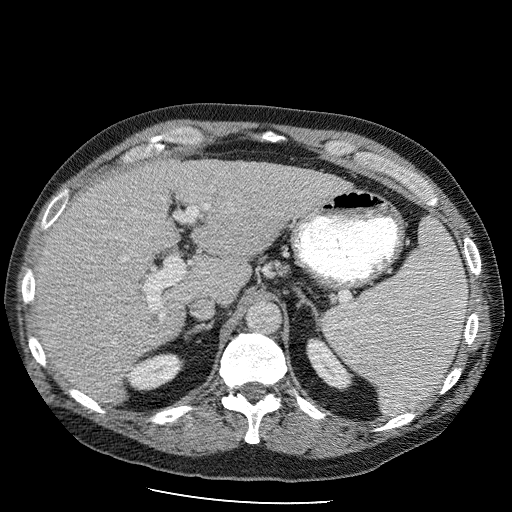
Contrast-enhanced abdominal CT (liver protocol), one axial slice; position 65 of 98 along the scan axis; reconstruction kernel STANDARD; 120 kVp; soft-tissue window (W 400 / L 40 HU); 2.5 mm slice thickness; 512 × 512 image matrix, field of view 400 × 400 mm. Case-level facts recorded for this patient, not image findings: diagnosis: hepatocellular carcinoma (patient treated with transarterial chemoembolisation; whether this scan precedes or follows treatment is not stated here); TNM stage (as recorded): Stage-II; Child-Pugh class: B.
Annotated regions visible in this slice (semi-automatically segmented with operator editing):
- liver parenchyma outside the tumour (the mass and vessels are separate outlines, so this box may not span the whole liver): bounding box <35,158,354,406> (left, top, right, bottom; pixels)
- liver vessels: <66,209,205,372>